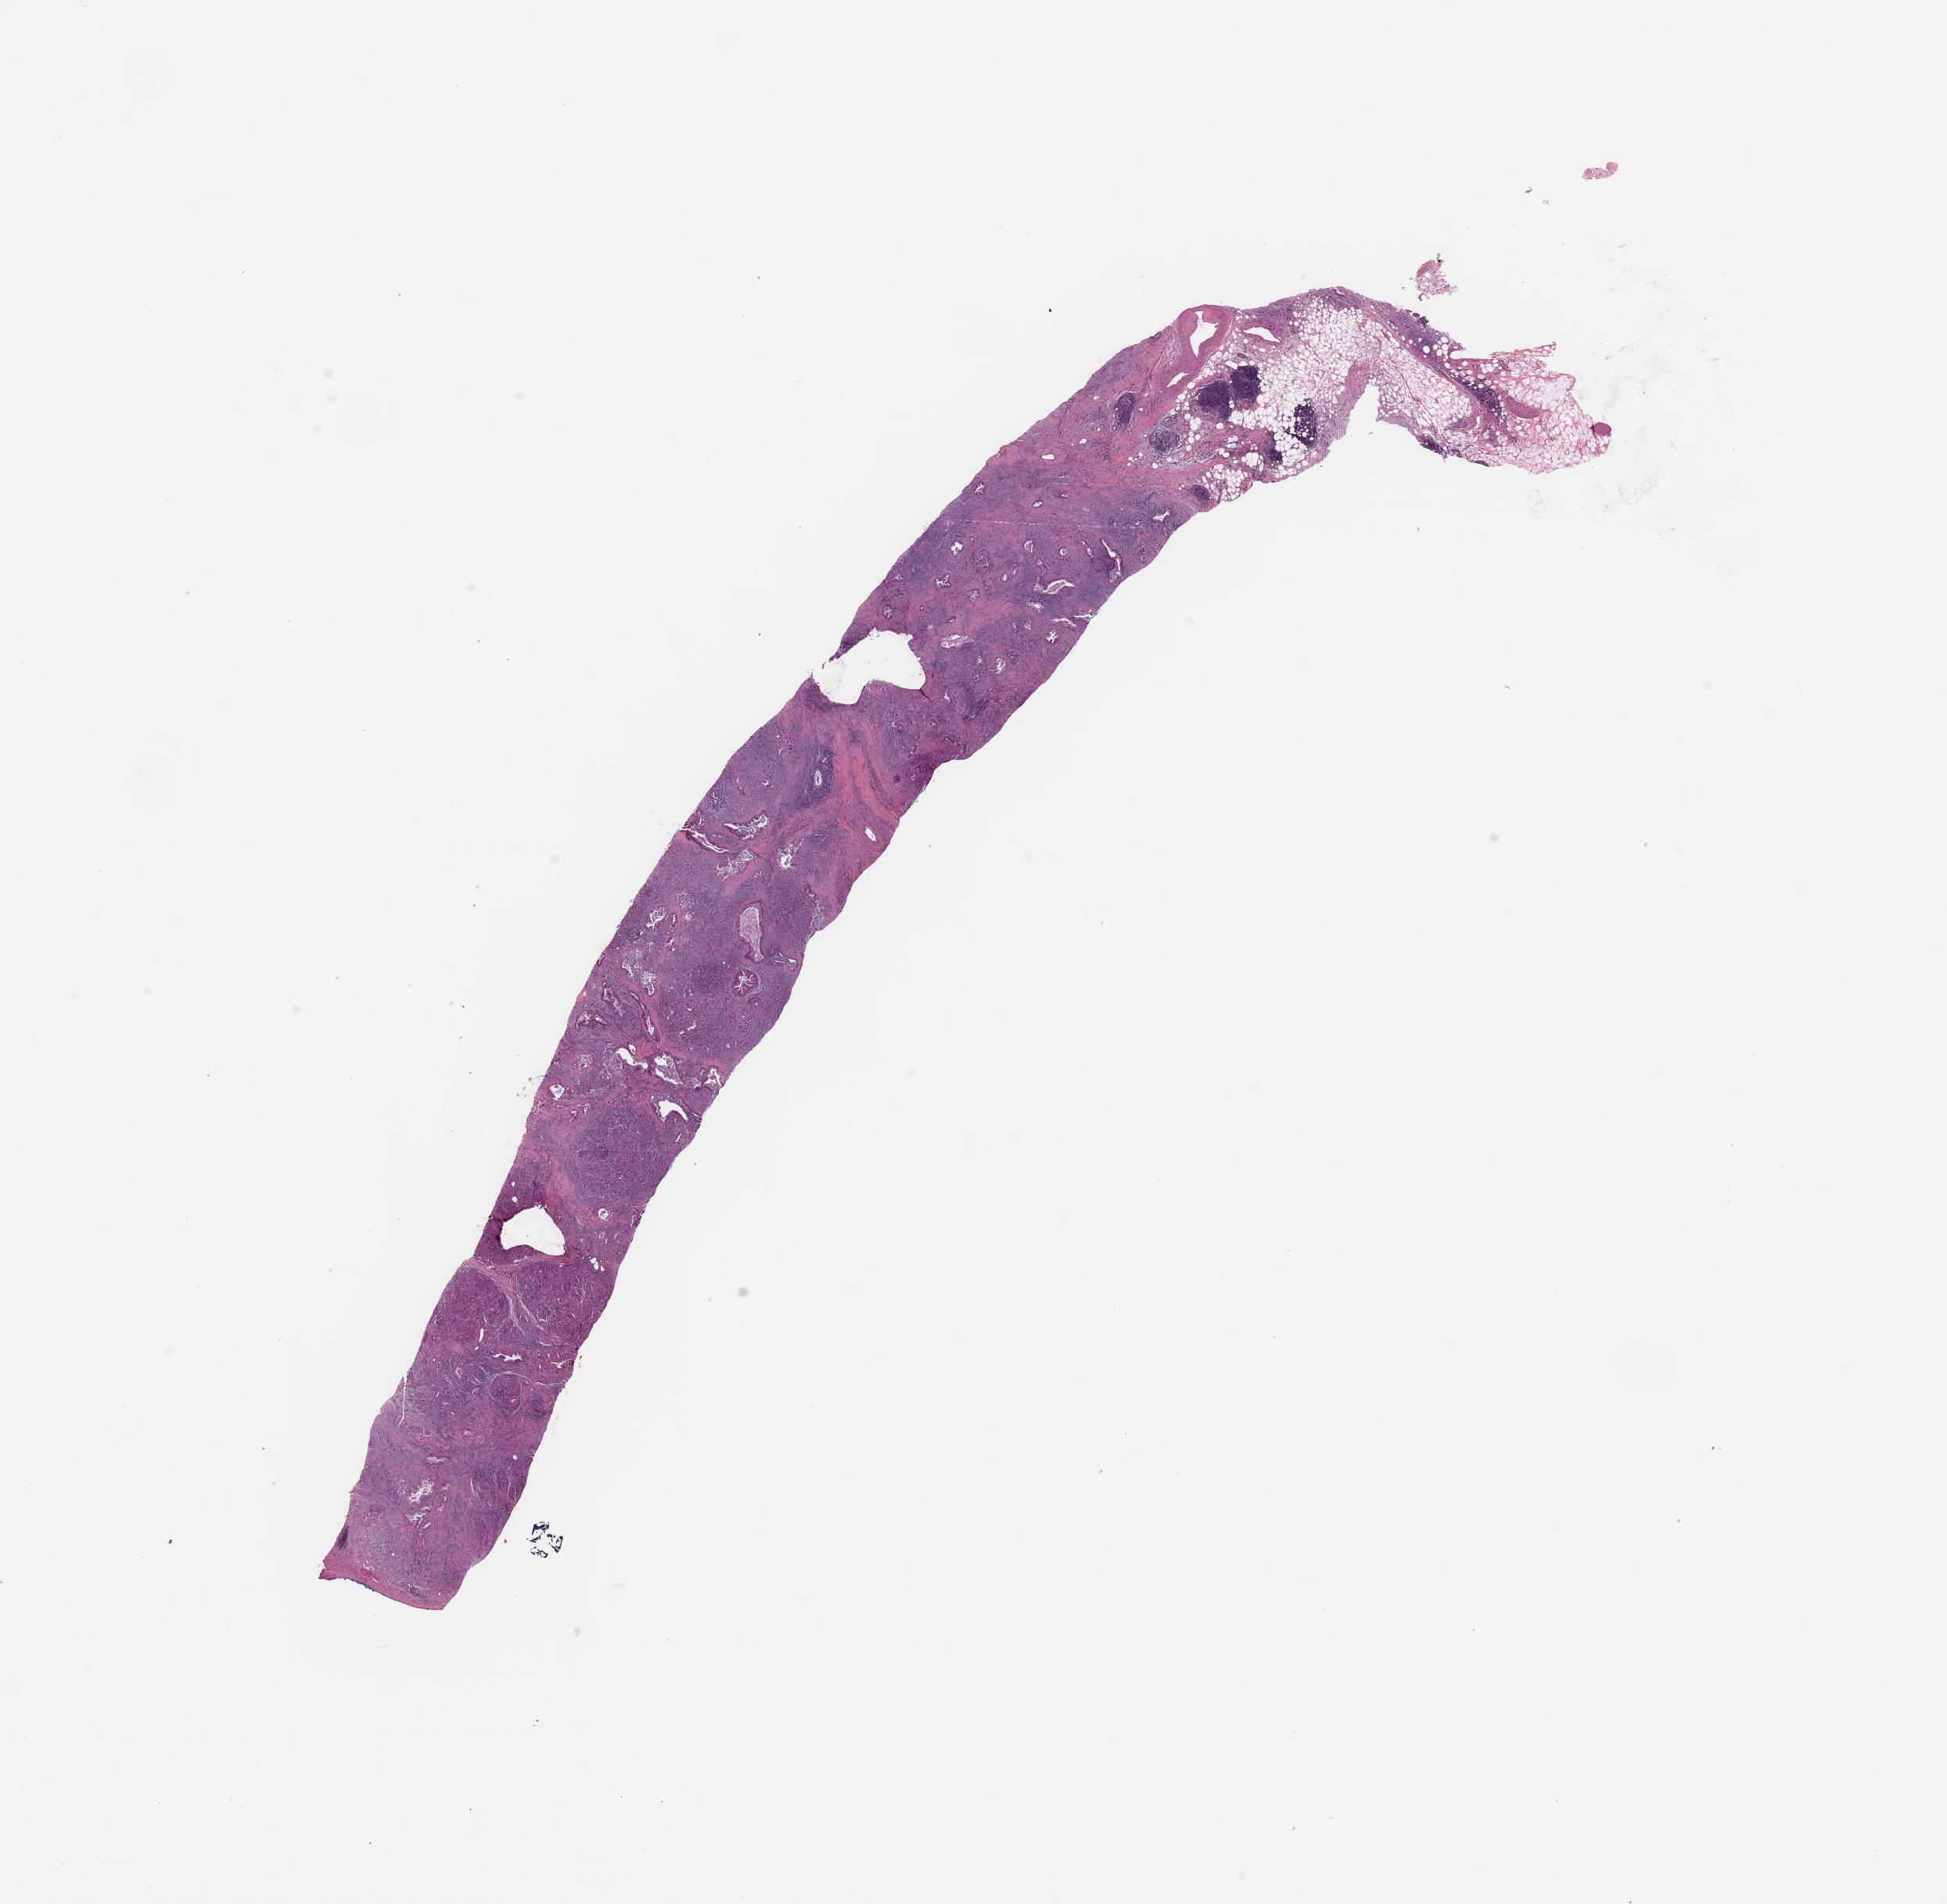
Digitized H&E tissue section (whole slide) — whole scanned area (about 19.7 x 19.3 mm) shown as a low-resolution overview. Tumour tissue sample, sampled site: pancreas. 80-year-old male patient. Histologic grade: G2 (moderately differentiated). Pathologist review of this section (percent, as recorded): tumour nuclei 20%, necrosis 0%.
AJCC pathologic stage: IIB. Diagnosis: Infiltrating duct carcinoma, NOS. Primary tumour site (as recorded): head.